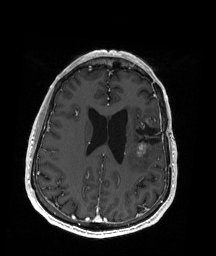
Brain MRI from a brain-tumour surgery series, one axial slice; position 72 of 192 along the scan axis; T1-weighted post-contrast; 1 mm slice thickness; 216 × 256 image matrix, field of view 211 × 250 mm. From the clinical record (not read from this slice): histopathology: Oligodendroglioma; WHO grade: 2; IDH mutation: yes.
Outlined on this slice (expert manual segmentation):
- previous resection cavity: box from (x=132, y=121) to (x=163, y=148) px
- tumour: (x=136, y=117)–(x=154, y=155)